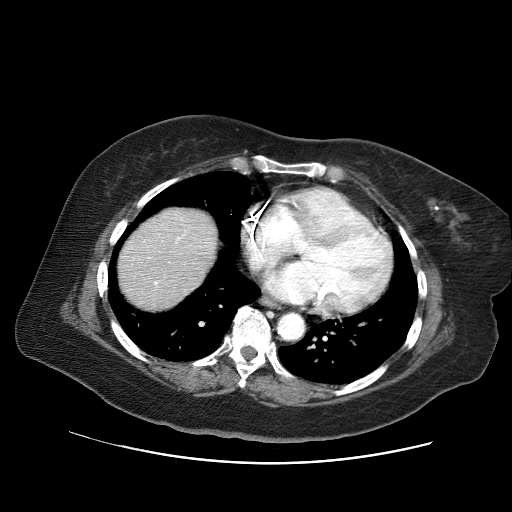
Contrast-enhanced abdominal CT (liver protocol), one axial slice; slice 63 of 71 in the series (ordered by position); reconstruction kernel STANDARD; soft-tissue window (W 400 / L 40 HU); 2.5 mm slice thickness; 512 × 512 image matrix, field of view 400 × 400 mm. Case-level facts recorded for this patient, not image findings: diagnosis: hepatocellular carcinoma (patient treated with transarterial chemoembolisation; whether this scan precedes or follows treatment is not stated here); TNM stage (as recorded): Stage-II; Child-Pugh class: A; tumour nodularity: multinodular.
Outlined on this slice (semi-automatic segmentation, software-assisted and operator-edited):
- abdominal aorta: bounding box <278,313,303,338> (left, top, right, bottom; pixels)
- liver parenchyma outside the tumour (the mass and vessels are separate outlines, so this box may not span the whole liver): <118,206,216,308>
- liver vessels: <154,236,184,285>